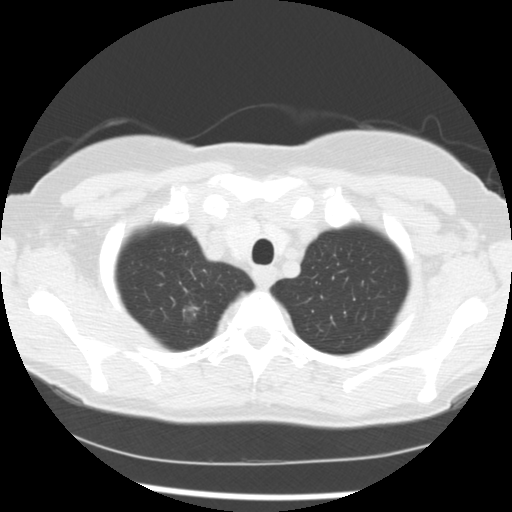
Chest CT (low-dose screening protocol), one axial image, first (baseline) screen, lung window (W 1500 / L -600 HU), 2.5 mm slice thickness, standard (soft-tissue) reconstruction kernel (STANDARD), slice 24 of 241 in the series, 512 × 512 image matrix, field of view 320 × 320 mm. Female participant, aged 60 years at enrolment. Former smoker at enrolment.
Lesion marked by an expert reader, bounding box <167,291,212,331> (left, top, right, bottom; pixels). The screening reader recorded 3 non-calcified nodules or masses ≥4 mm on this exam (right upper lobe, right middle lobe, left lower lobe); which of them this box marks is not recorded.